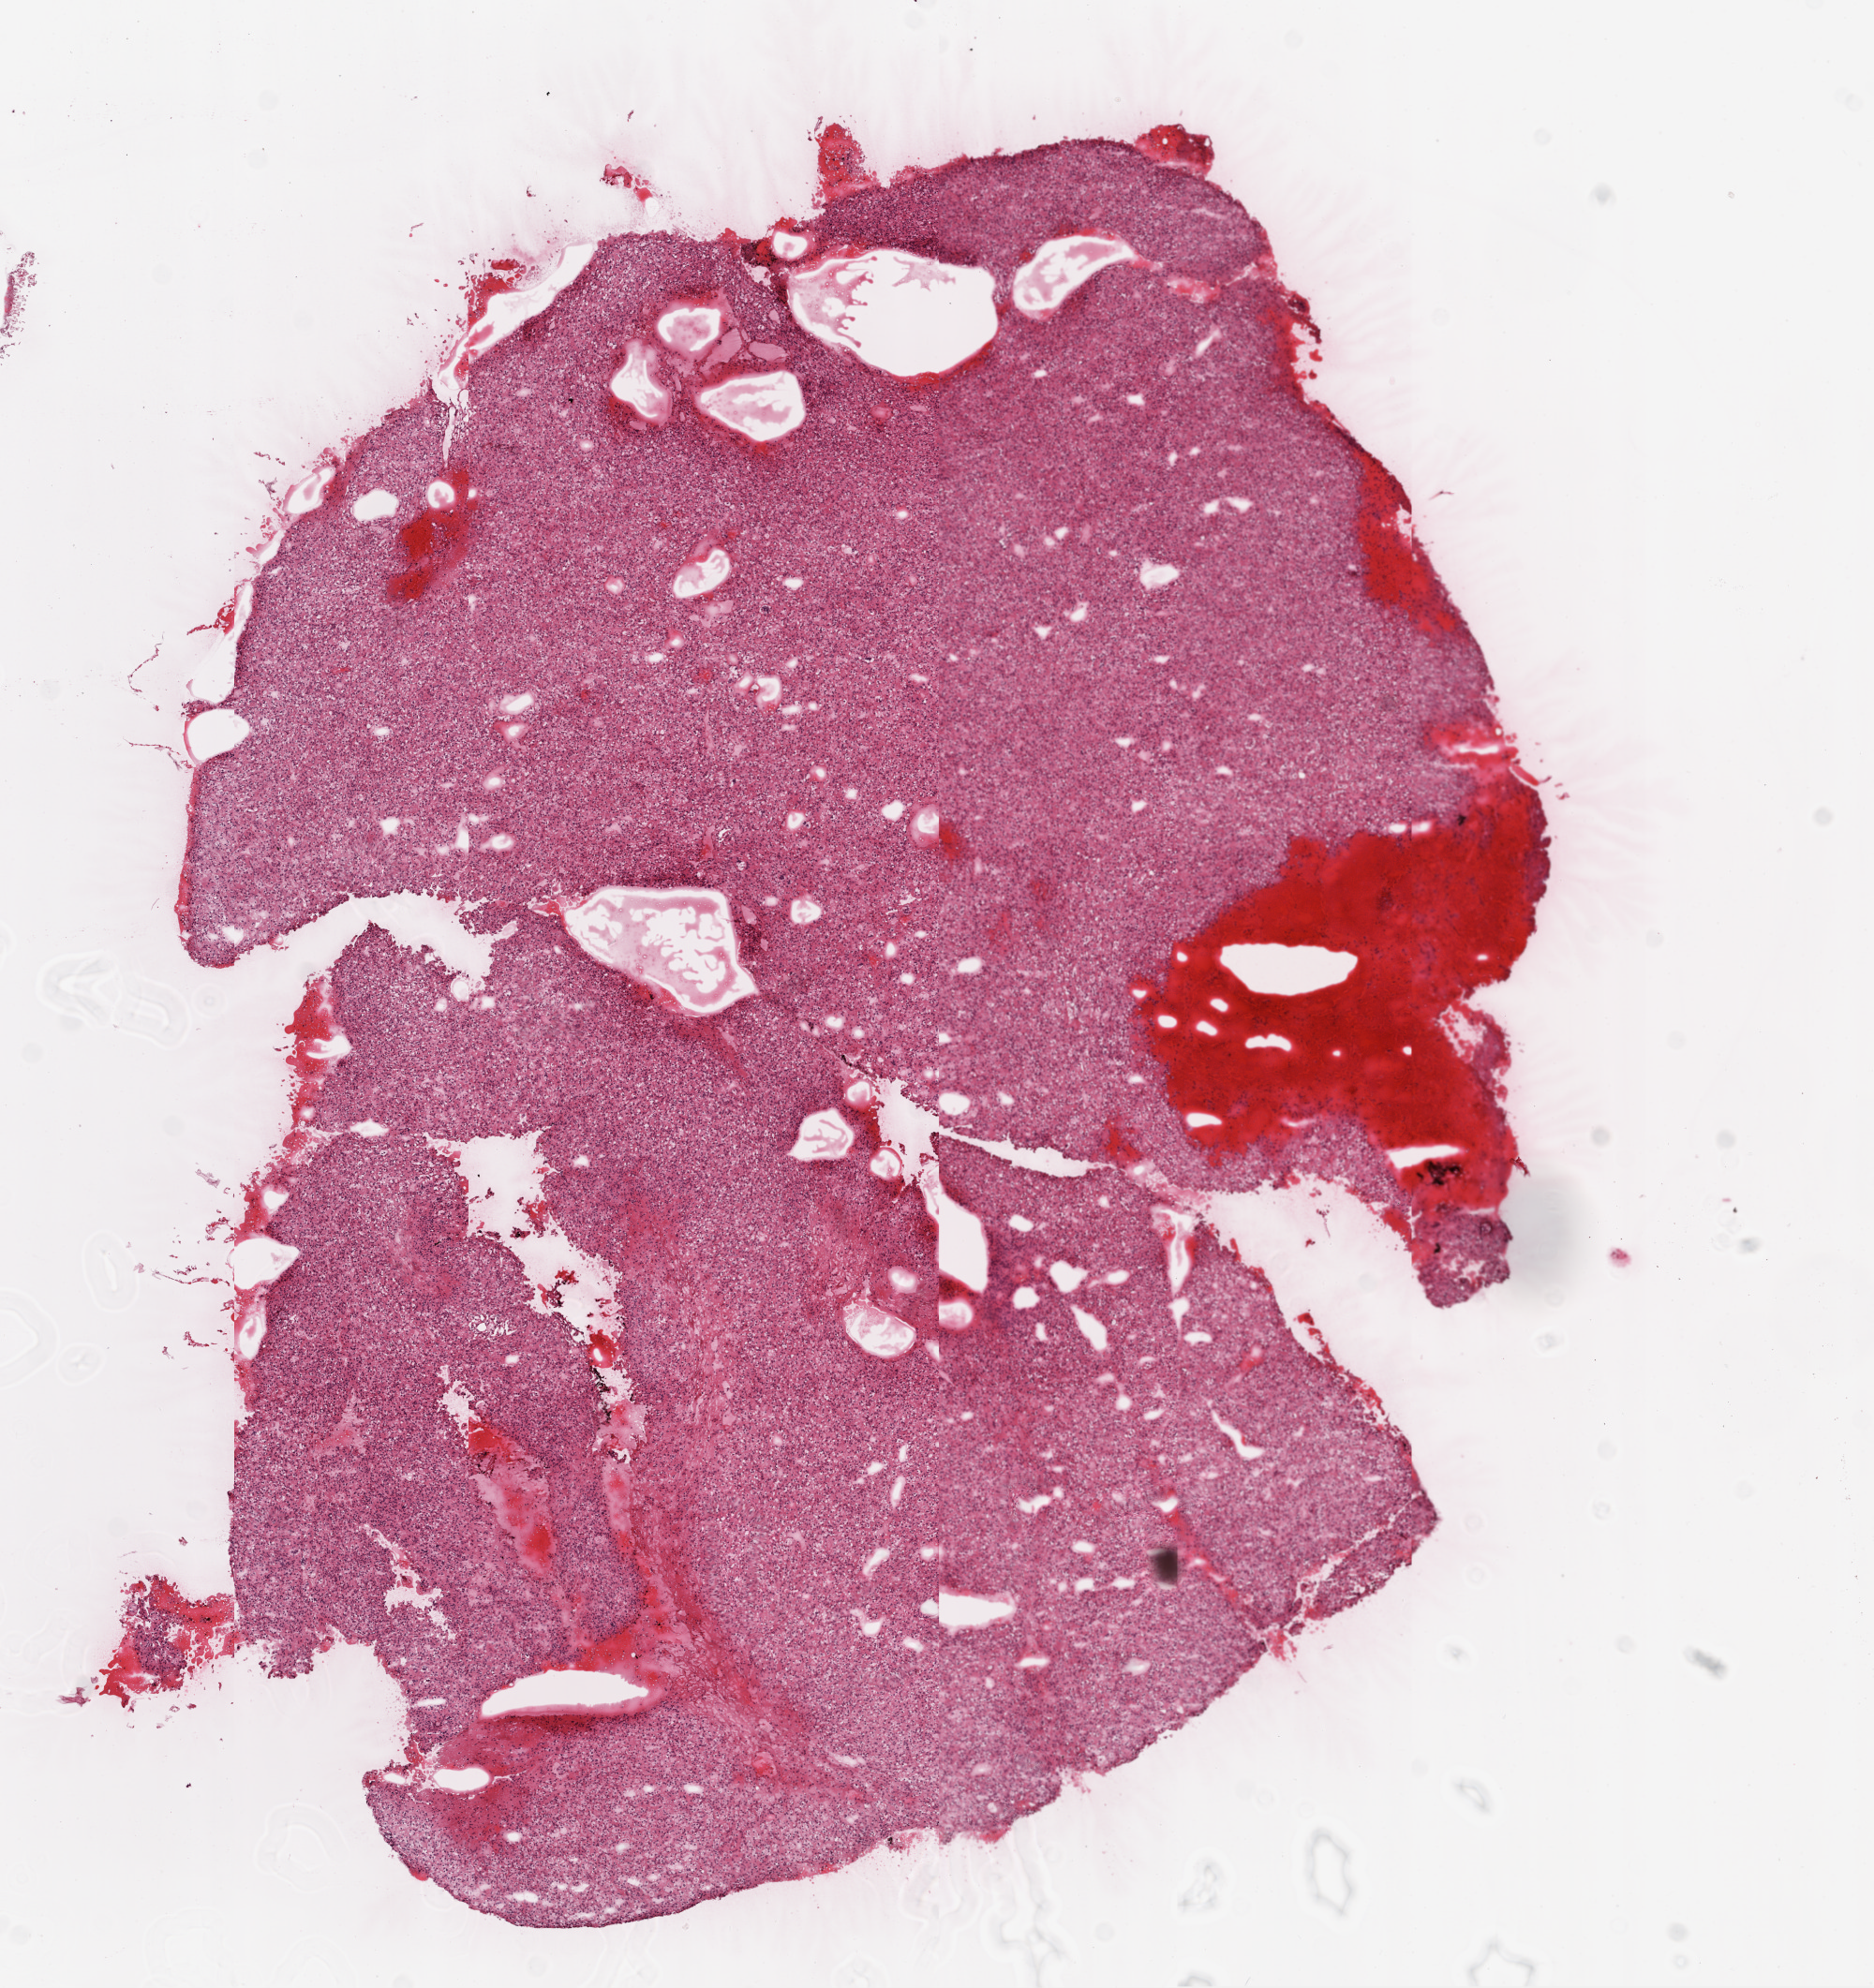
Whole-slide histology image, Hematoxylin and eosin (H&E) stained — a low-resolution overview of the entire scanned area, about 8.0 x 8.5 mm (acquisition: 20x scan). Frozen section from the top of the tissue portion. Primary tumour sample from the kidney. Male, age 61 years at initial diagnosis. Histologic grade: G2 (moderately differentiated). Slide review estimates, as recorded: tumour cells 90%, tumour nuclei 85%, normal cells 0%, stromal cells 10%, necrosis 0%.
TNM: T1a N0 M0. AJCC pathologic stage: I. Histologic diagnosis: Clear cell adenocarcinoma, NOS. Lymph nodes positive (case pathology): 0 of 2 examined.